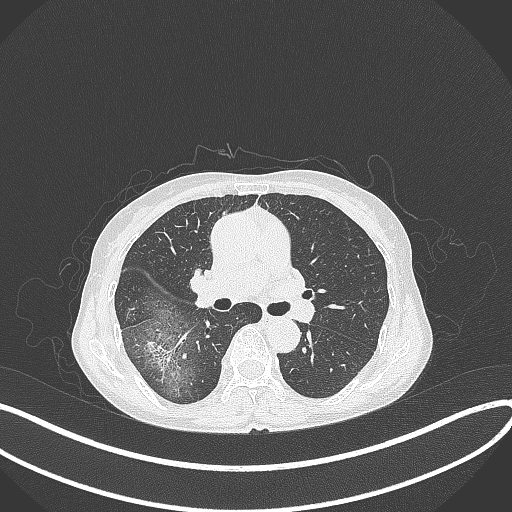
Chest CT, one axial slice; slice 232 of 371 in the series (ordered by position); reconstruction kernel B70f; lung window (W 1500 / L -600 HU); 1 mm slice thickness; 512 × 512 image matrix, field of view 400 × 400 mm. Female patient, age 69 years. Case-level facts recorded for this patient, not image findings: clinical TNM (as recorded): T1b N0 M0; histopathological grade: G2-3.
Structures marked on this image (rectangle marked by the reading radiologist):
- lung tumour (recorded histology: adenocarcinoma): box from (x=142, y=336) to (x=174, y=379) px